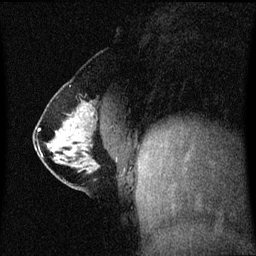
Breast MRI (dynamic contrast-enhanced), one sagittal slice. Slice 24 of 60 in the series (ordered by position). Dynamic contrast-enhanced series, image 2 of 3 at this slice position (ordered by acquisition). 1.5 T. TE 4.2 ms, TR 8.4 ms. 2 mm slice thickness. 256 × 256 image matrix. Patient: female, 40 years. From the clinical record (not read from this slice): setting: breast cancer imaged before/during neoadjuvant chemotherapy; receptor status: triple-negative.
Annotated regions visible in this slice (semi-automatic segmentation, software-assisted and operator-edited):
- analysis volume of interest (the breast-tissue region the enhancement analysis was run in; not a lesion): bounding box (x1, y1, x2, y2) in pixels: (34, 112, 113, 188)
- tumour enhancement mask (voxels above the 70 % enhancement threshold inside the analysis volume of interest): (39, 130, 61, 142)